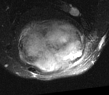
MRI of an extremity soft-tissue mass, one axial slice. Slice 27 of 52 in the series (ordered by position). T2-weighted fat-saturated. MR volume resampled by the dataset authors to the PET/CT grid (not the native acquisition matrix). 3.27 mm slice thickness. 109 × 95 image matrix, field of view 106 × 93 mm. Male patient. From the clinical record (not read from this slice): histological type: synovial sarcoma; site of the primary tumour: left poplietal fossa.
Outlined on this slice (expert contour drawn on MRI and transferred to this co-registered scan by the dataset authors):
- gross tumour volume (mass): bounding box <15,17,86,73> (left, top, right, bottom; pixels)